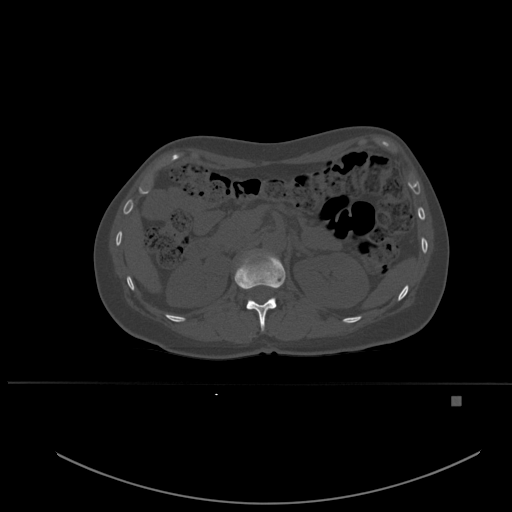
CT including the spine, one axial slice; position 249 of 651 along the scan axis; bone window (W 1800 / L 400 HU); 512 × 512 image matrix. Patient: female, 49 years. From the clinical record (not read from this slice): primary cancer: breast.
Structures marked on this image (semi-automatic segmentation, software-assisted and operator-edited):
- T12 vertebra: bounding box (x1, y1, x2, y2) in pixels: (234, 253, 286, 331)